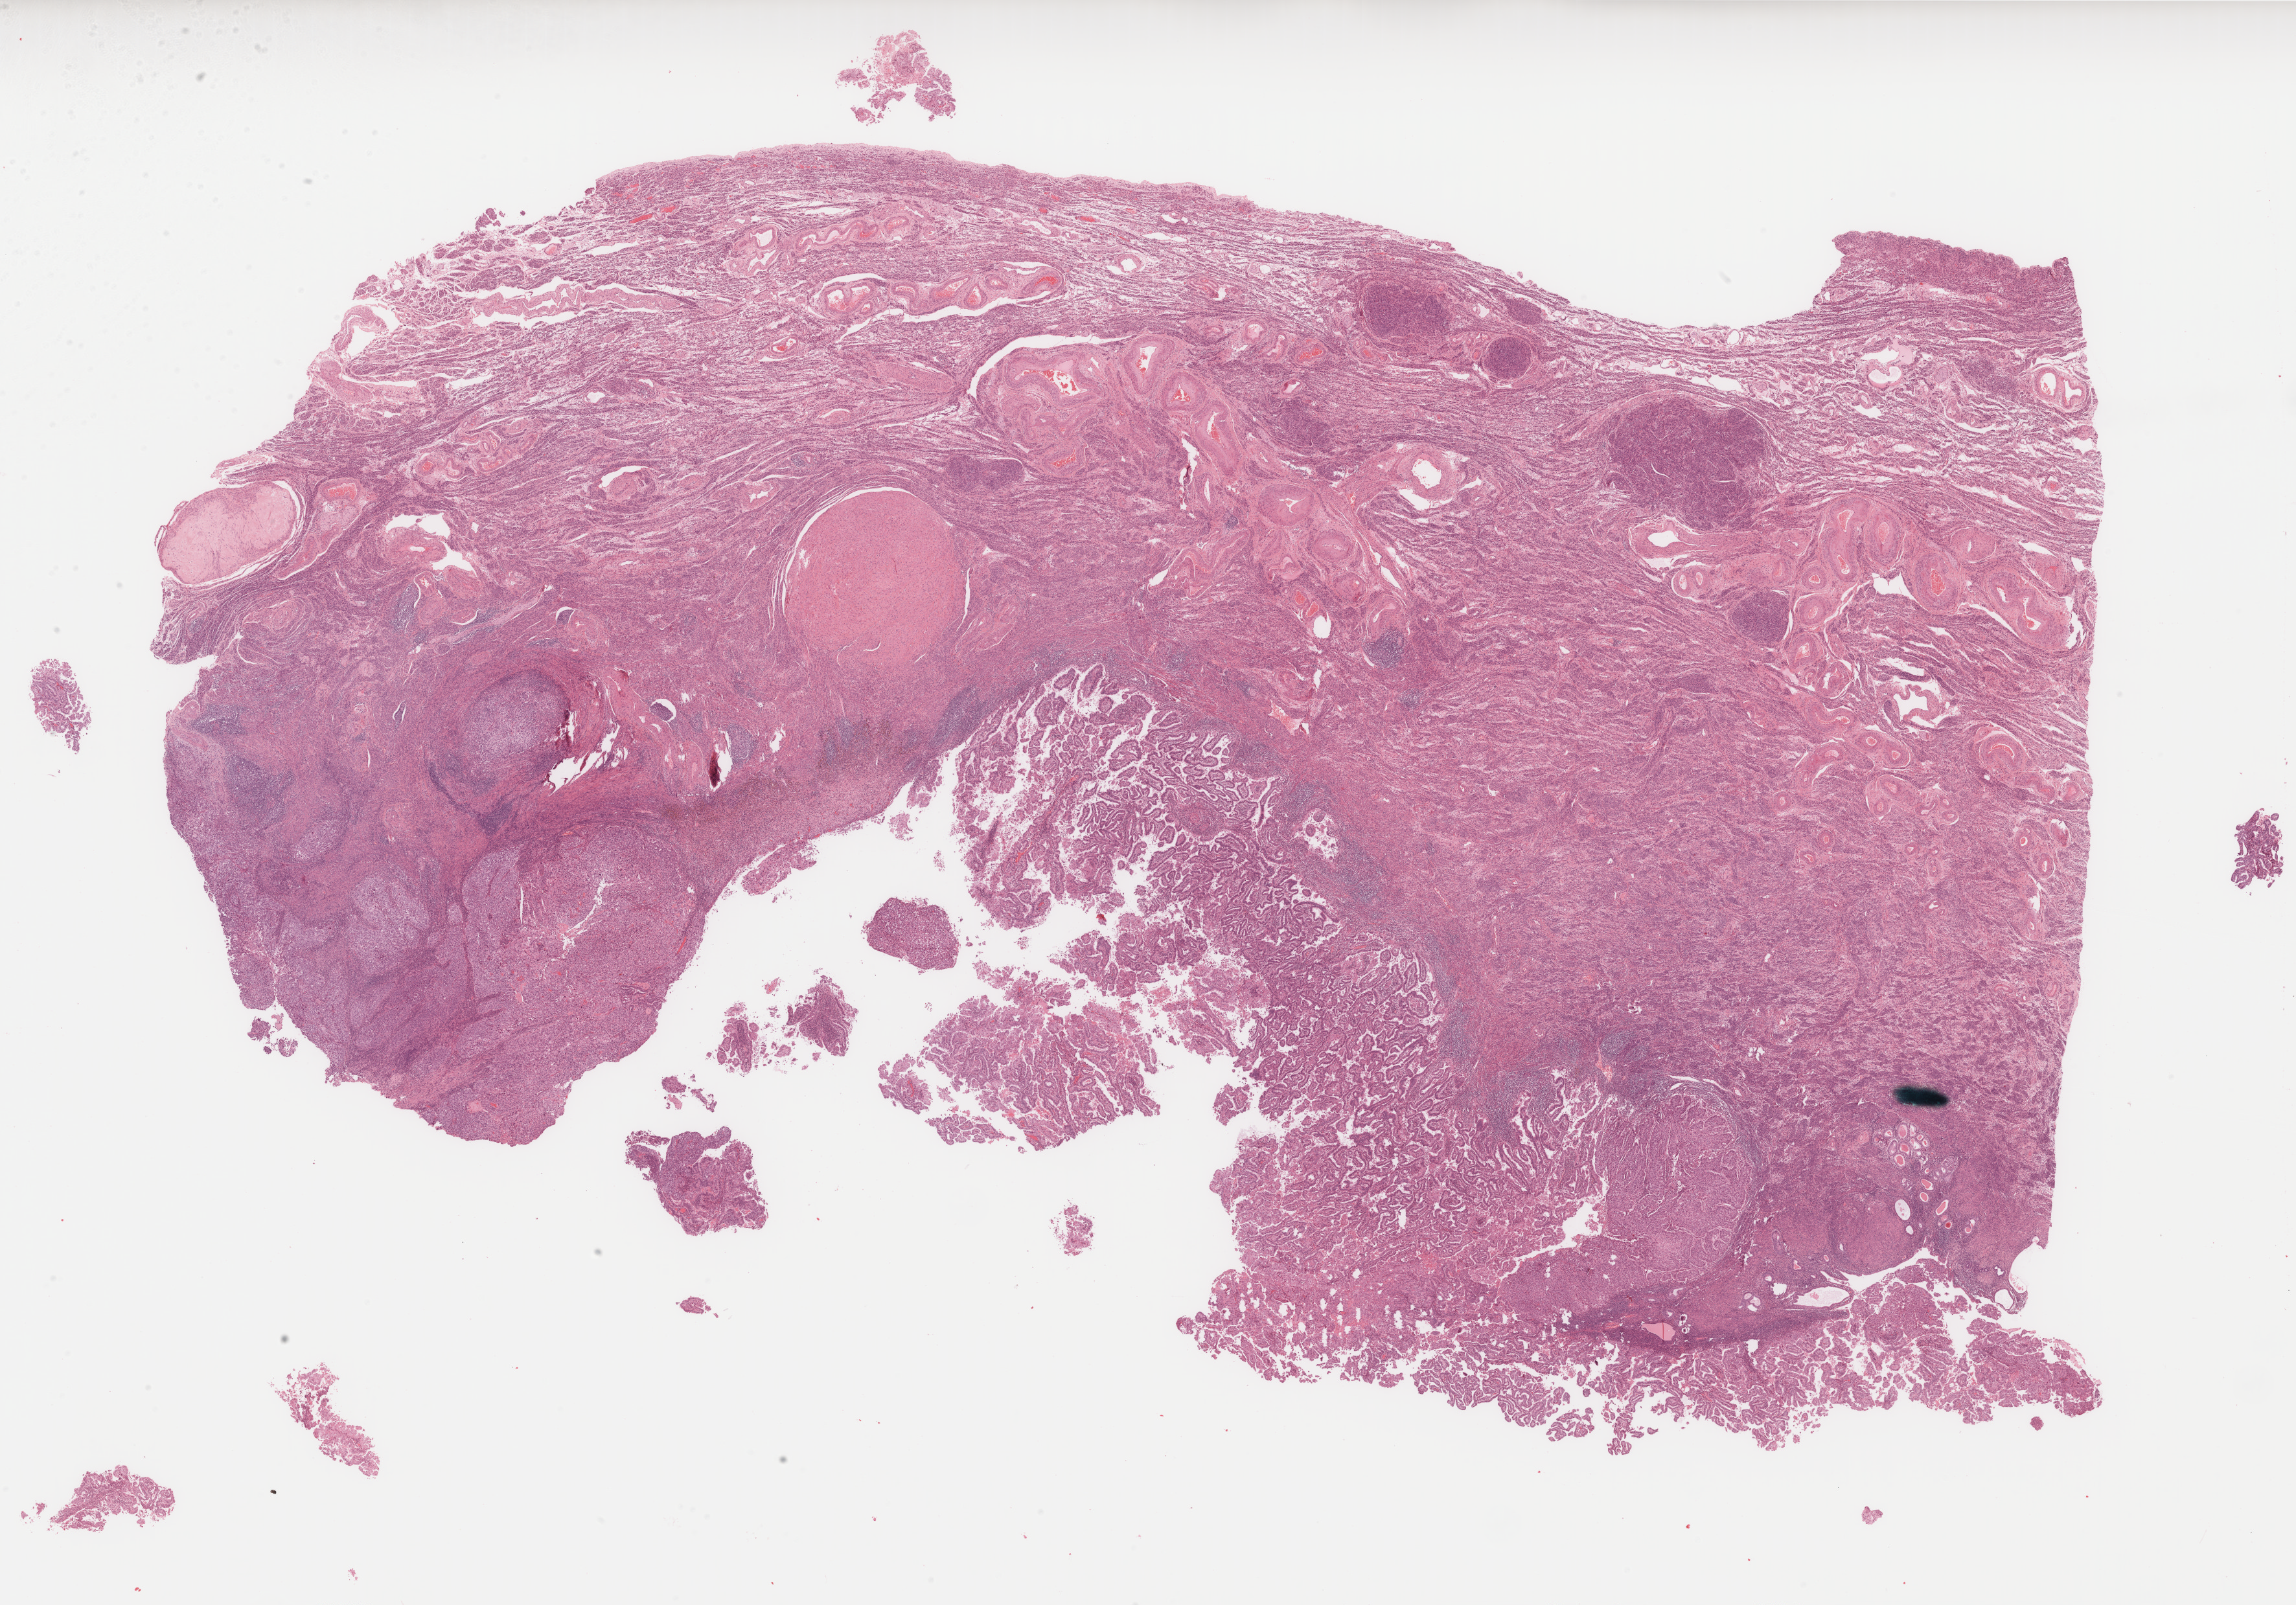
Digitized Hematoxylin and eosin (H&E) stained tissue section (whole slide) — low-resolution overview of the scanned area, about 28.6 x 20.0 mm. Formalin-fixed paraffin-embedded (FFPE) diagnostic section. Sample: primary tumour, uterus. Female patient; age at initial diagnosis 83 years. Histologic grade: G3 (poorly differentiated).
Diagnosis: Endometrioid adenocarcinoma, NOS (endometrium). FIGO stage: IB.